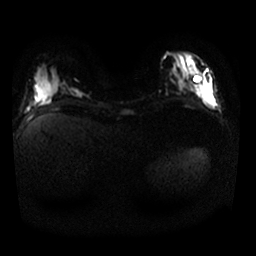
Breast MRI, one axial slice; slice 10 of 25 in the series (ordered by position); diffusion-weighted series; image 2 of 4 stored at this slice position (different b-values; order by instance number); 1.5 T; 256 × 256 image matrix. Female patient.
Structures marked on this image (expert manual segmentation):
- tumour on diffusion-weighted imaging: box from (x=199, y=80) to (x=211, y=98) px